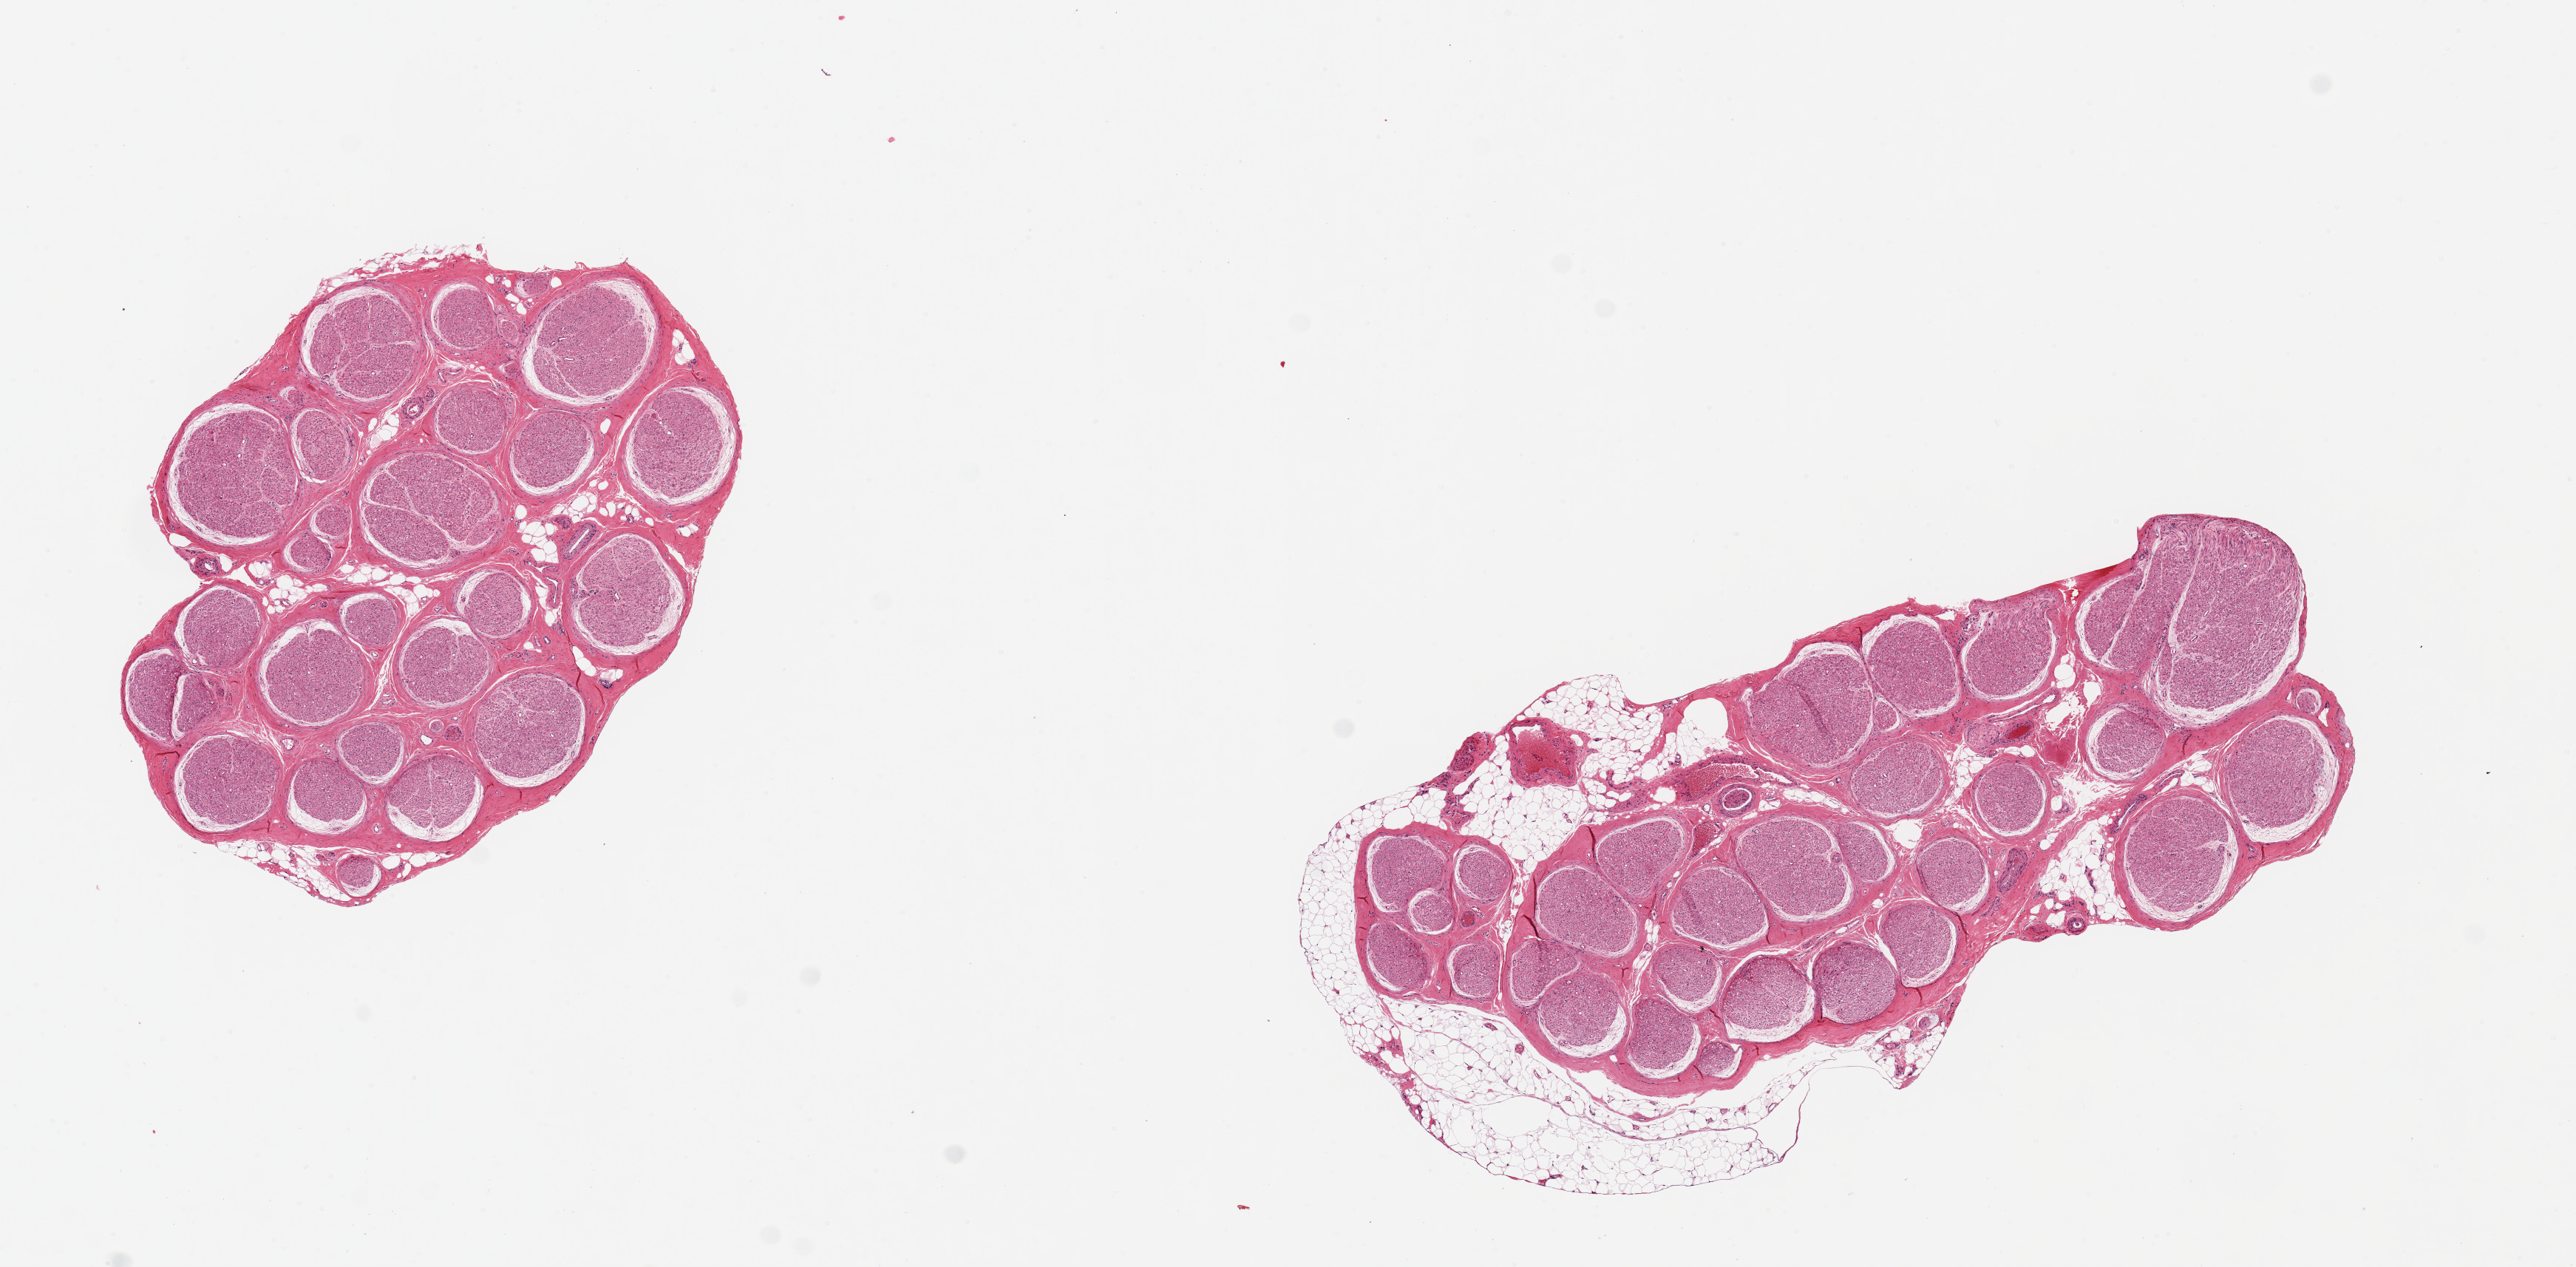
Whole-slide image, haematoxylin and eosin stain, low-resolution overview of the scanned area, about 13.8 x 6.8 mm (from a 20x scan). PAXgene-fixed, paraffin-embedded tissue. Sampled site (target tissue): tibial nerve. Donor tissue sample. Donor: male.
* reviewer comment on this tissue sample: 2 pieces ~3mm d. Relatively clean, focal discontinuous adherent fat ~0.5mm thick on one